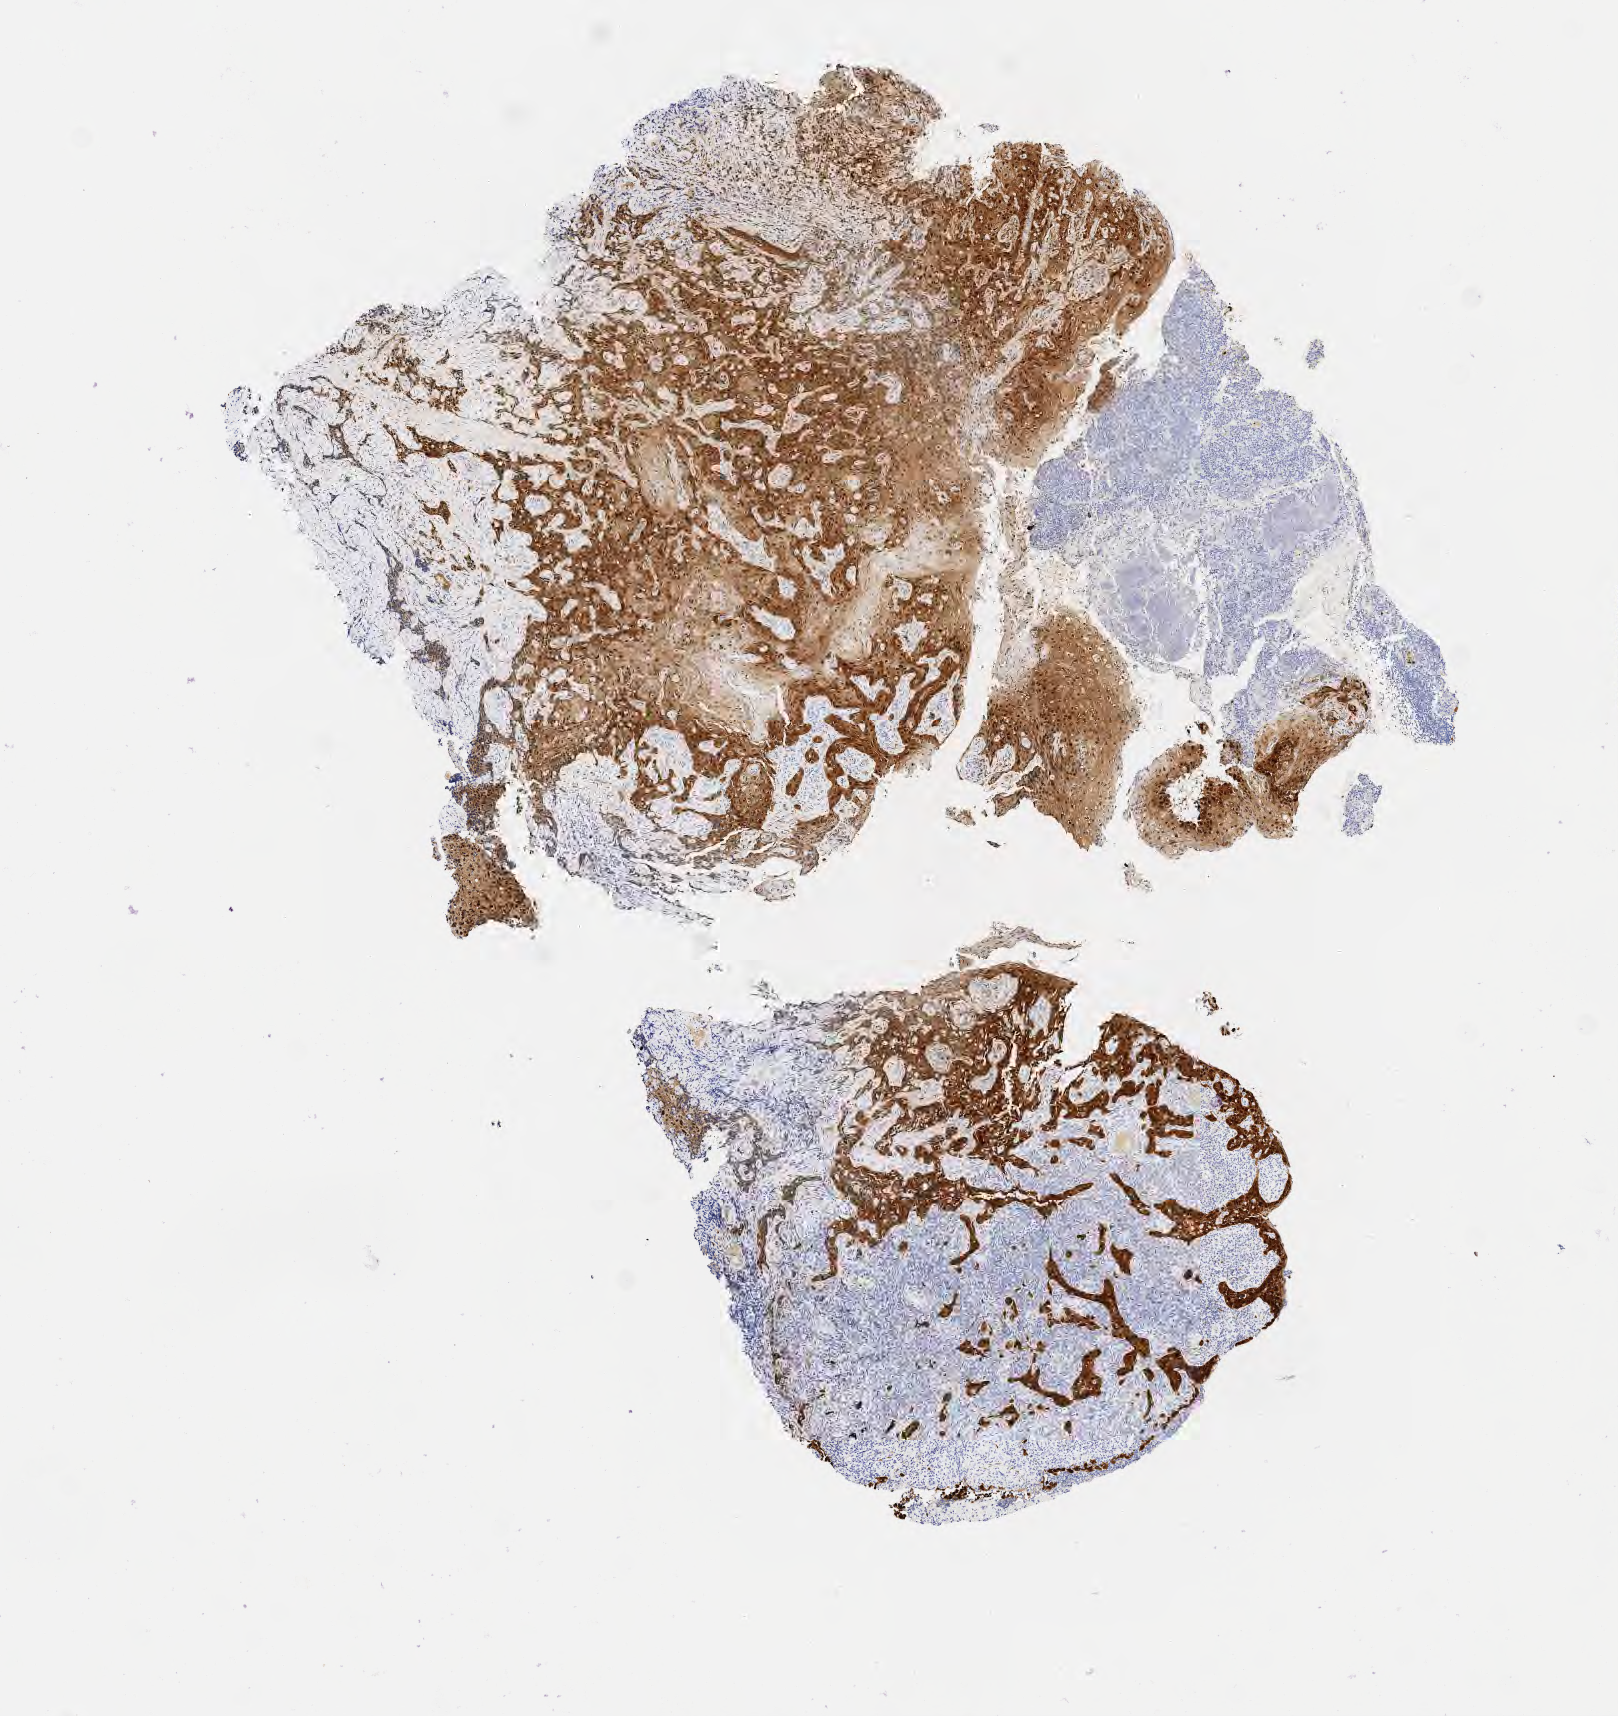
Immunohistochemistry (IHC) whole-slide image stained for p16 (p16INK4a), shown as a low-resolution overview of the whole scanned area (about 6.5 x 6.9 mm). Specimen: tumor tissue. Site: cervix. Female patient, aged 41.
Diagnosis: Squamous cell carcinoma, keratinizing, NOS.